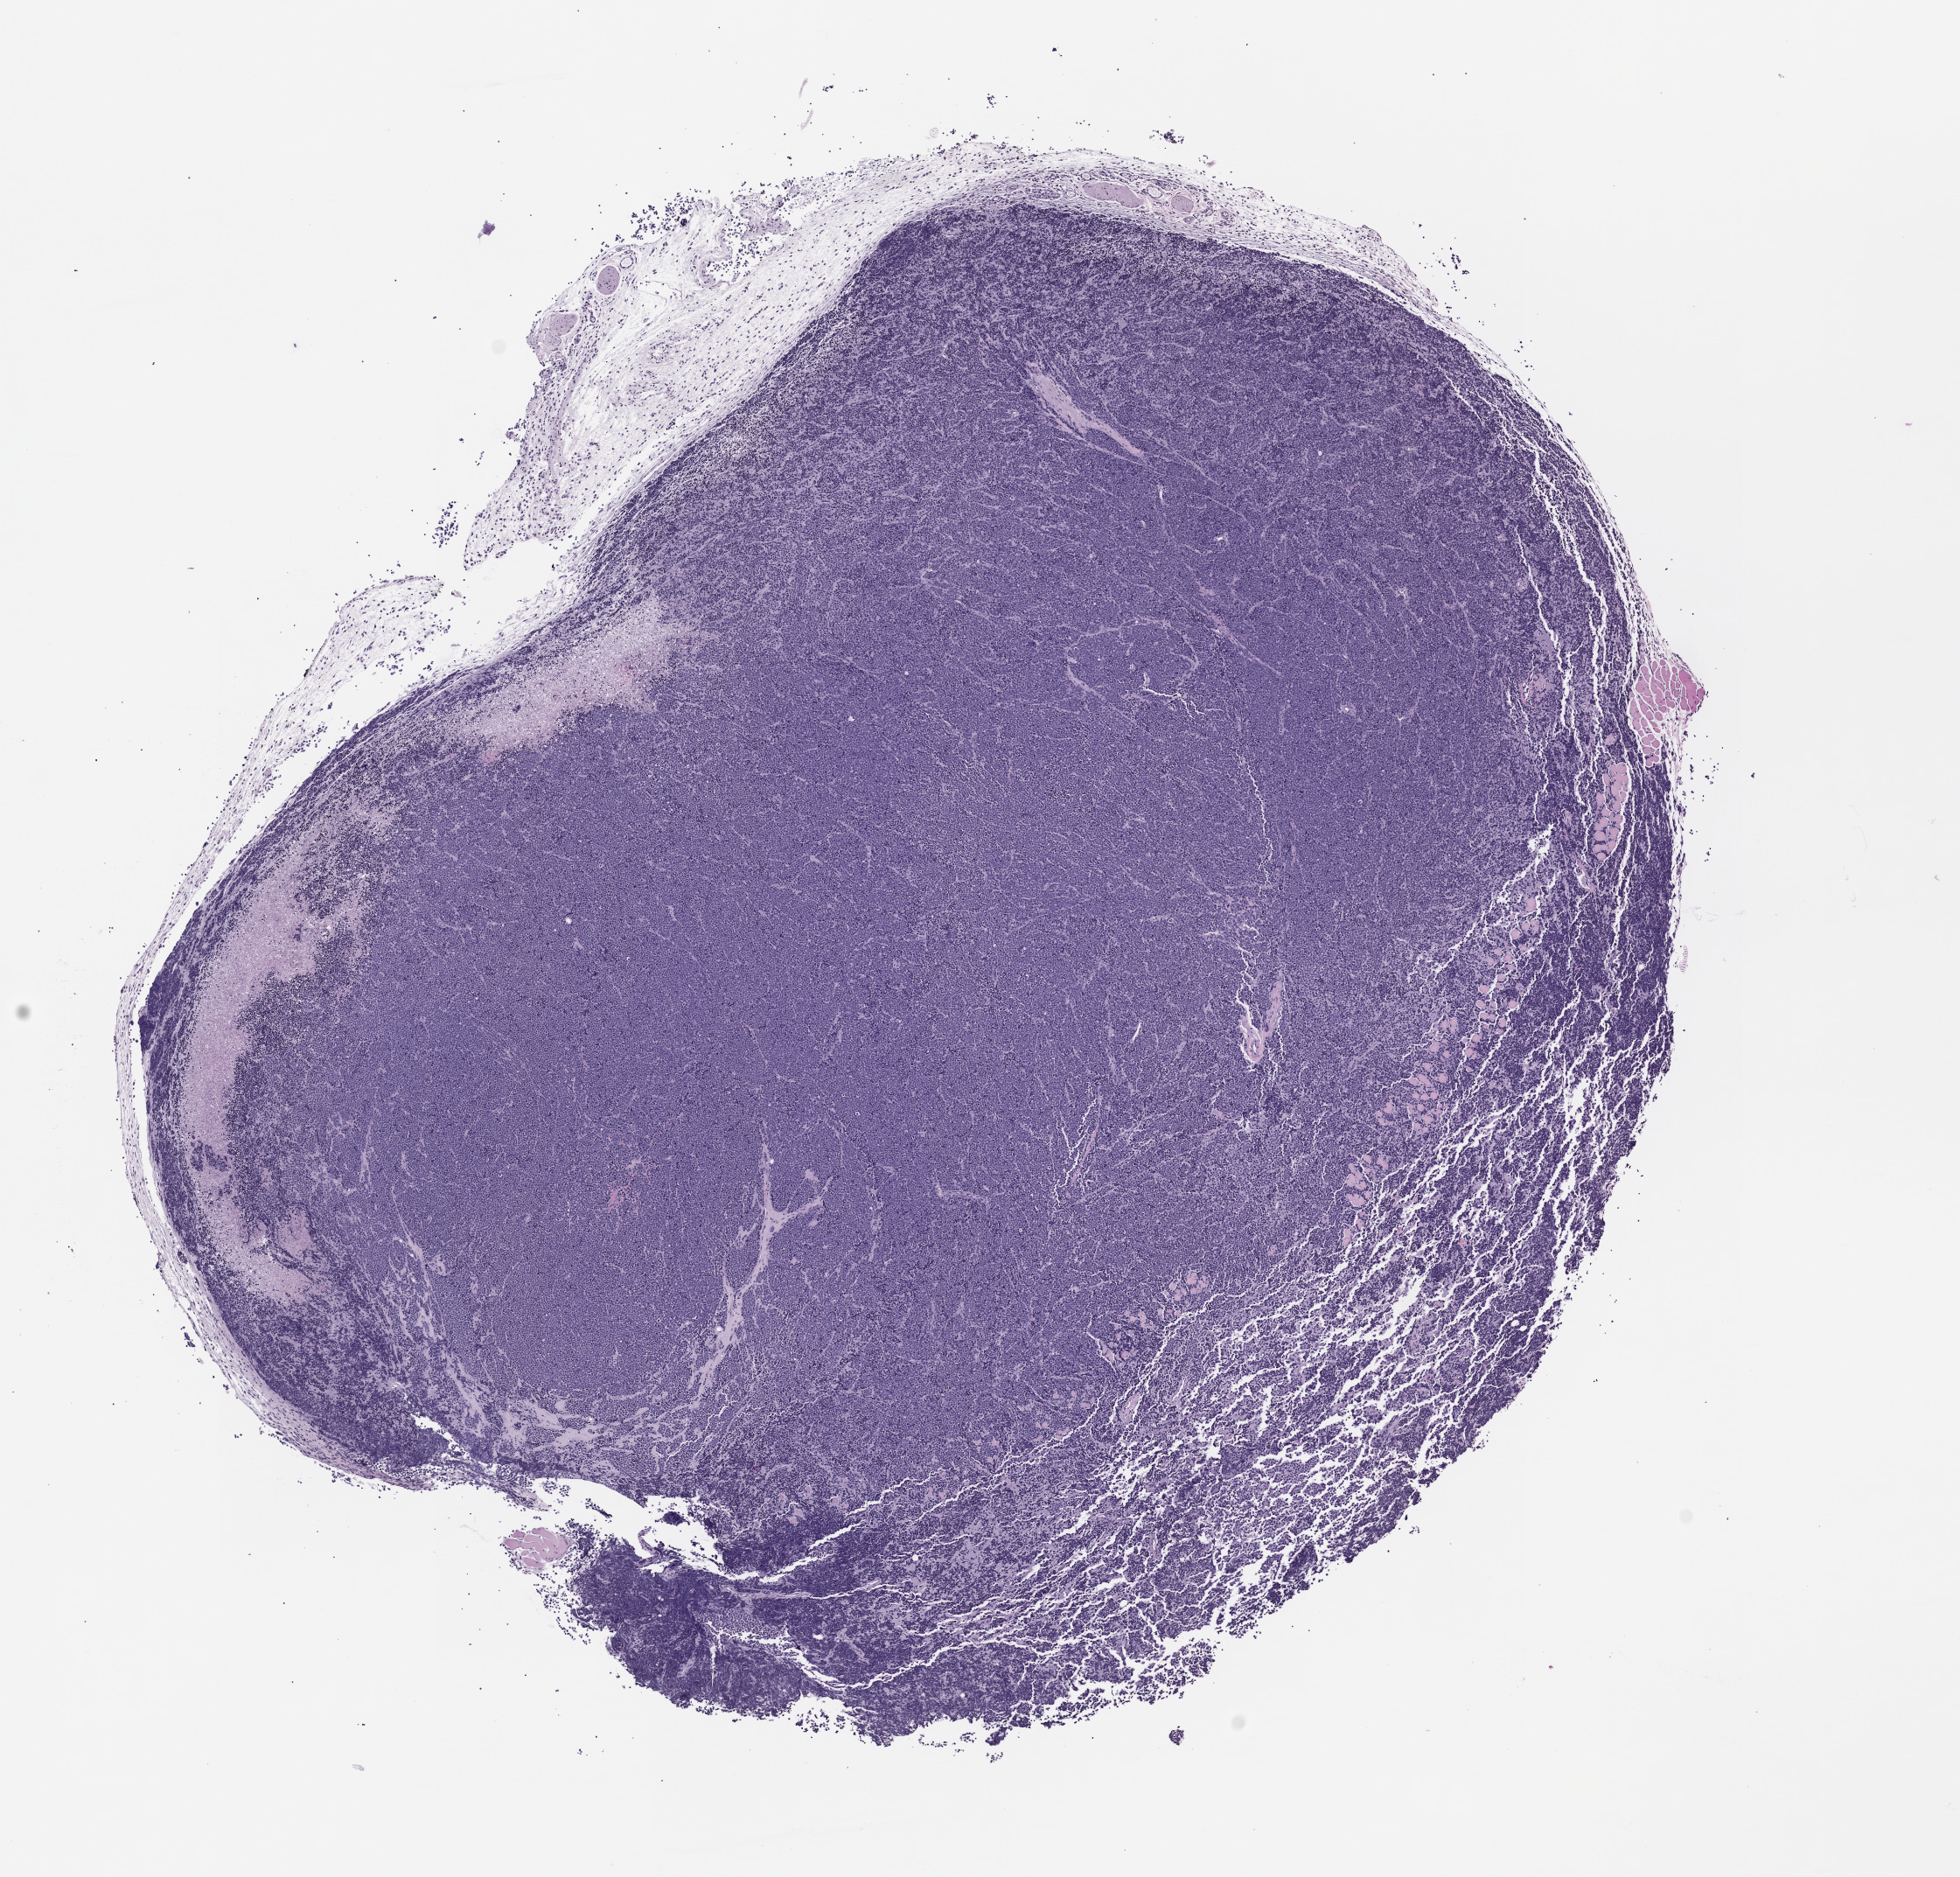
Whole-slide image, hematoxylin and eosin (H&E): patient-derived xenograft (human tumor grown in a mouse), passage 1 — whole scanned area (about 9.0 x 8.6 mm) shown as a low-resolution overview, formalin-fixed, paraffin-embedded (FFPE) tissue, originating tumor site category: lung.
Originating patient diagnosis: Lung Small Cell Carcinoma.